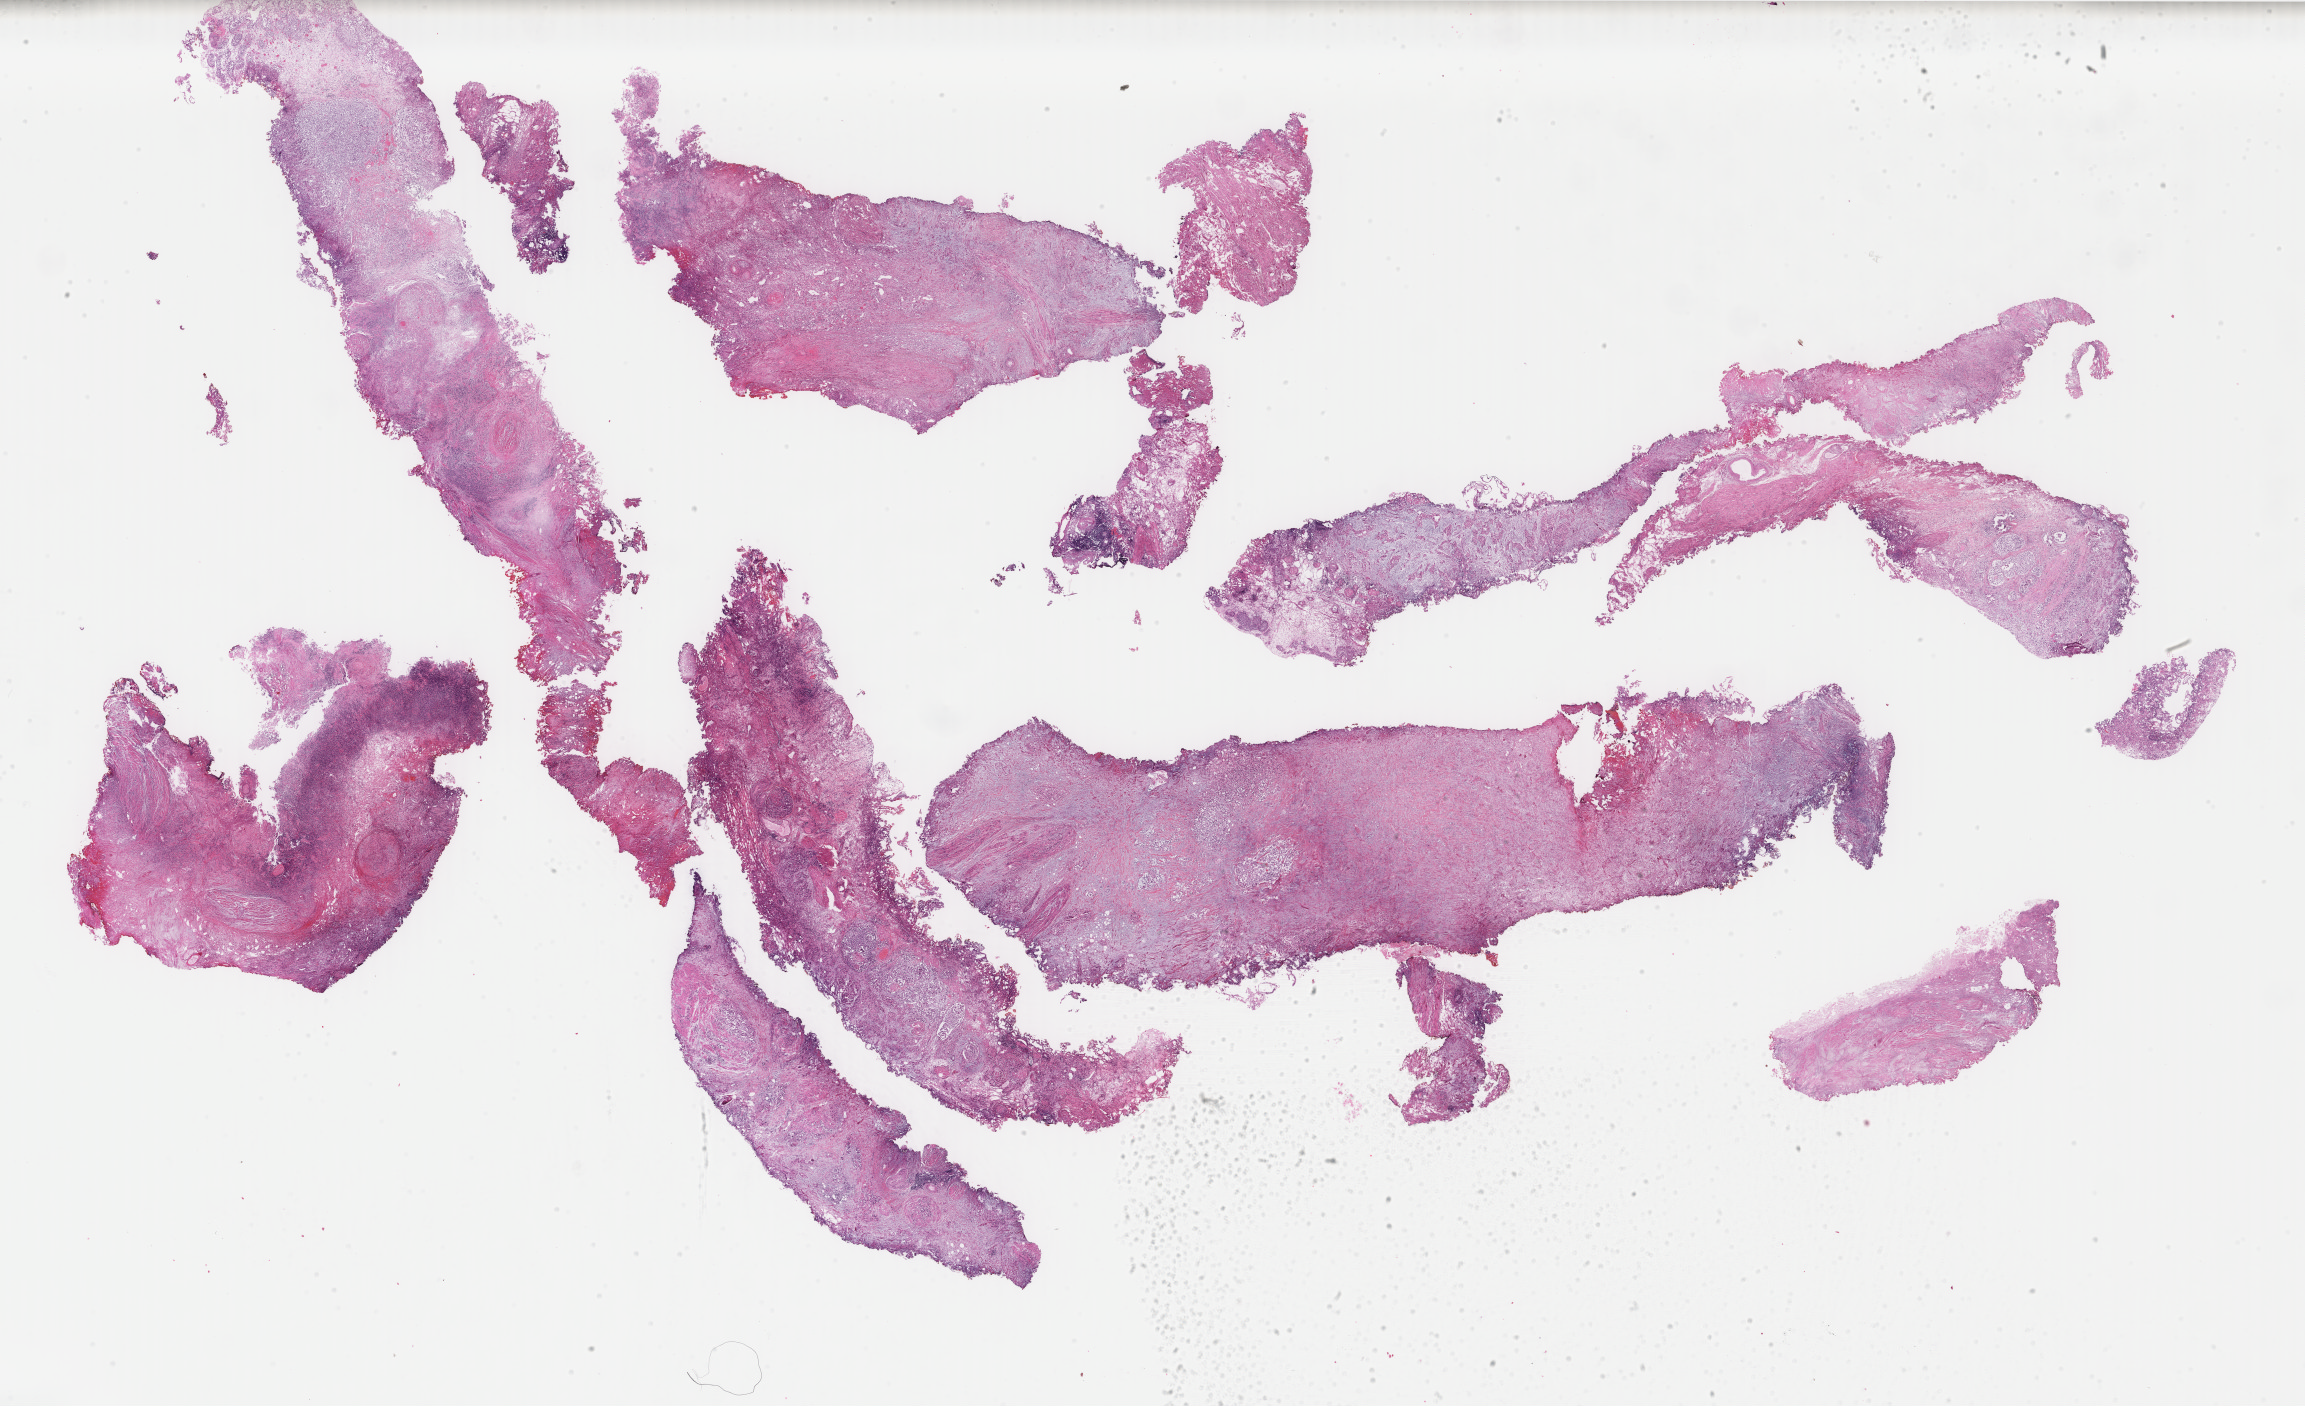
Digitized H&E-stained tissue section (whole slide) — a low-resolution overview of the entire scanned area, about 36.6 x 22.3 mm; formalin-fixed paraffin-embedded (FFPE) diagnostic section; bladder, primary tumour sample. Female, age 58 years at initial diagnosis. Histologic grade: high grade.
* AJCC pathologic stage: II (2nd edition)
* diagnosis: Transitional cell carcinoma
* TNM: N0 M0